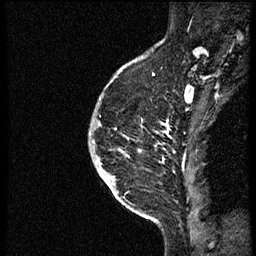
Breast MRI (dynamic contrast-enhanced), one sagittal slice; slice 44 of 56 in the series (ordered by position); dynamic contrast-enhanced study with each time point stored as its own series, time point 2 of 3 at this slice position (early post-contrast, ordered by acquisition time); 1.5 T; TE 4.2 ms, TR 21.3 ms; 256 × 256 image matrix, field of view 200 × 200 mm. Patient: female, 41 years. From the clinical record (not read from this slice): setting: breast cancer imaged before/during neoadjuvant chemotherapy; receptor status: HER2-positive.
Structures marked on this image (semi-automatic segmentation, software-assisted and operator-edited):
- analysis volume of interest (the breast-tissue region the enhancement analysis was run in; not a lesion): box from (x=98, y=73) to (x=177, y=205) px
- tumour enhancement mask (voxels above the 100 % enhancement threshold inside the analysis volume of interest): (x=106, y=123)–(x=169, y=180)